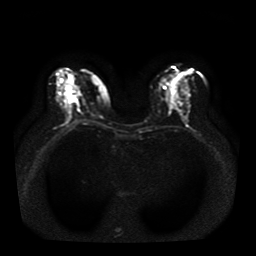
Breast MRI, one axial slice; slice 18 of 41 in the series (ordered by position); diffusion-weighted series; image 2 of 4 stored at this slice position (different b-values; order by instance number); 1.5 T; 5 mm slice thickness; 256 × 256 image matrix, field of view 330 × 330 mm. Female patient.
Structures marked on this image (manually delineated by an expert):
- tumour on diffusion-weighted imaging: bounding box [x1, y1, x2, y2] px = [67, 95, 75, 97]